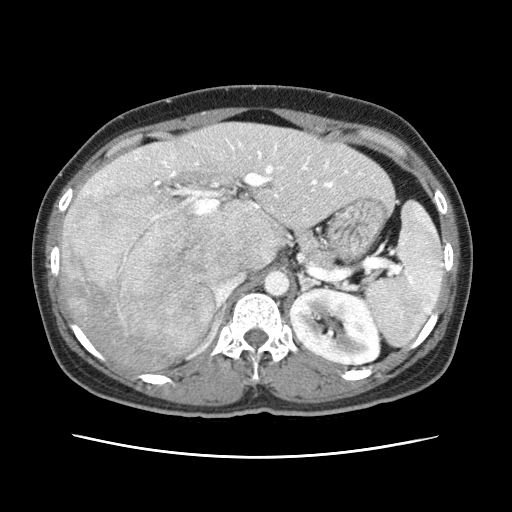
Contrast-enhanced abdominal CT (liver protocol), one axial slice; slice 37 of 79 in the series (ordered by position); 120 kVp; soft-tissue window (W 400 / L 40 HU); 512 × 512 image matrix, field of view 340 × 340 mm. From the clinical record (not read from this slice): diagnosis: hepatocellular carcinoma (patient treated with transarterial chemoembolisation; whether this scan precedes or follows treatment is not stated here); TNM stage (as recorded): Stage-I; Child-Pugh class: A; tumour differentiation: moderately differentiated.
Annotated regions visible in this slice (semi-automatically segmented with operator editing):
- abdominal aorta: bounding box <264,270,289,295> (left, top, right, bottom; pixels)
- liver parenchyma outside the tumour (the mass and vessels are separate outlines, so this box may not span the whole liver): <60,122,392,370>
- mass: <65,183,233,368>
- liver vessels: <86,139,361,214>